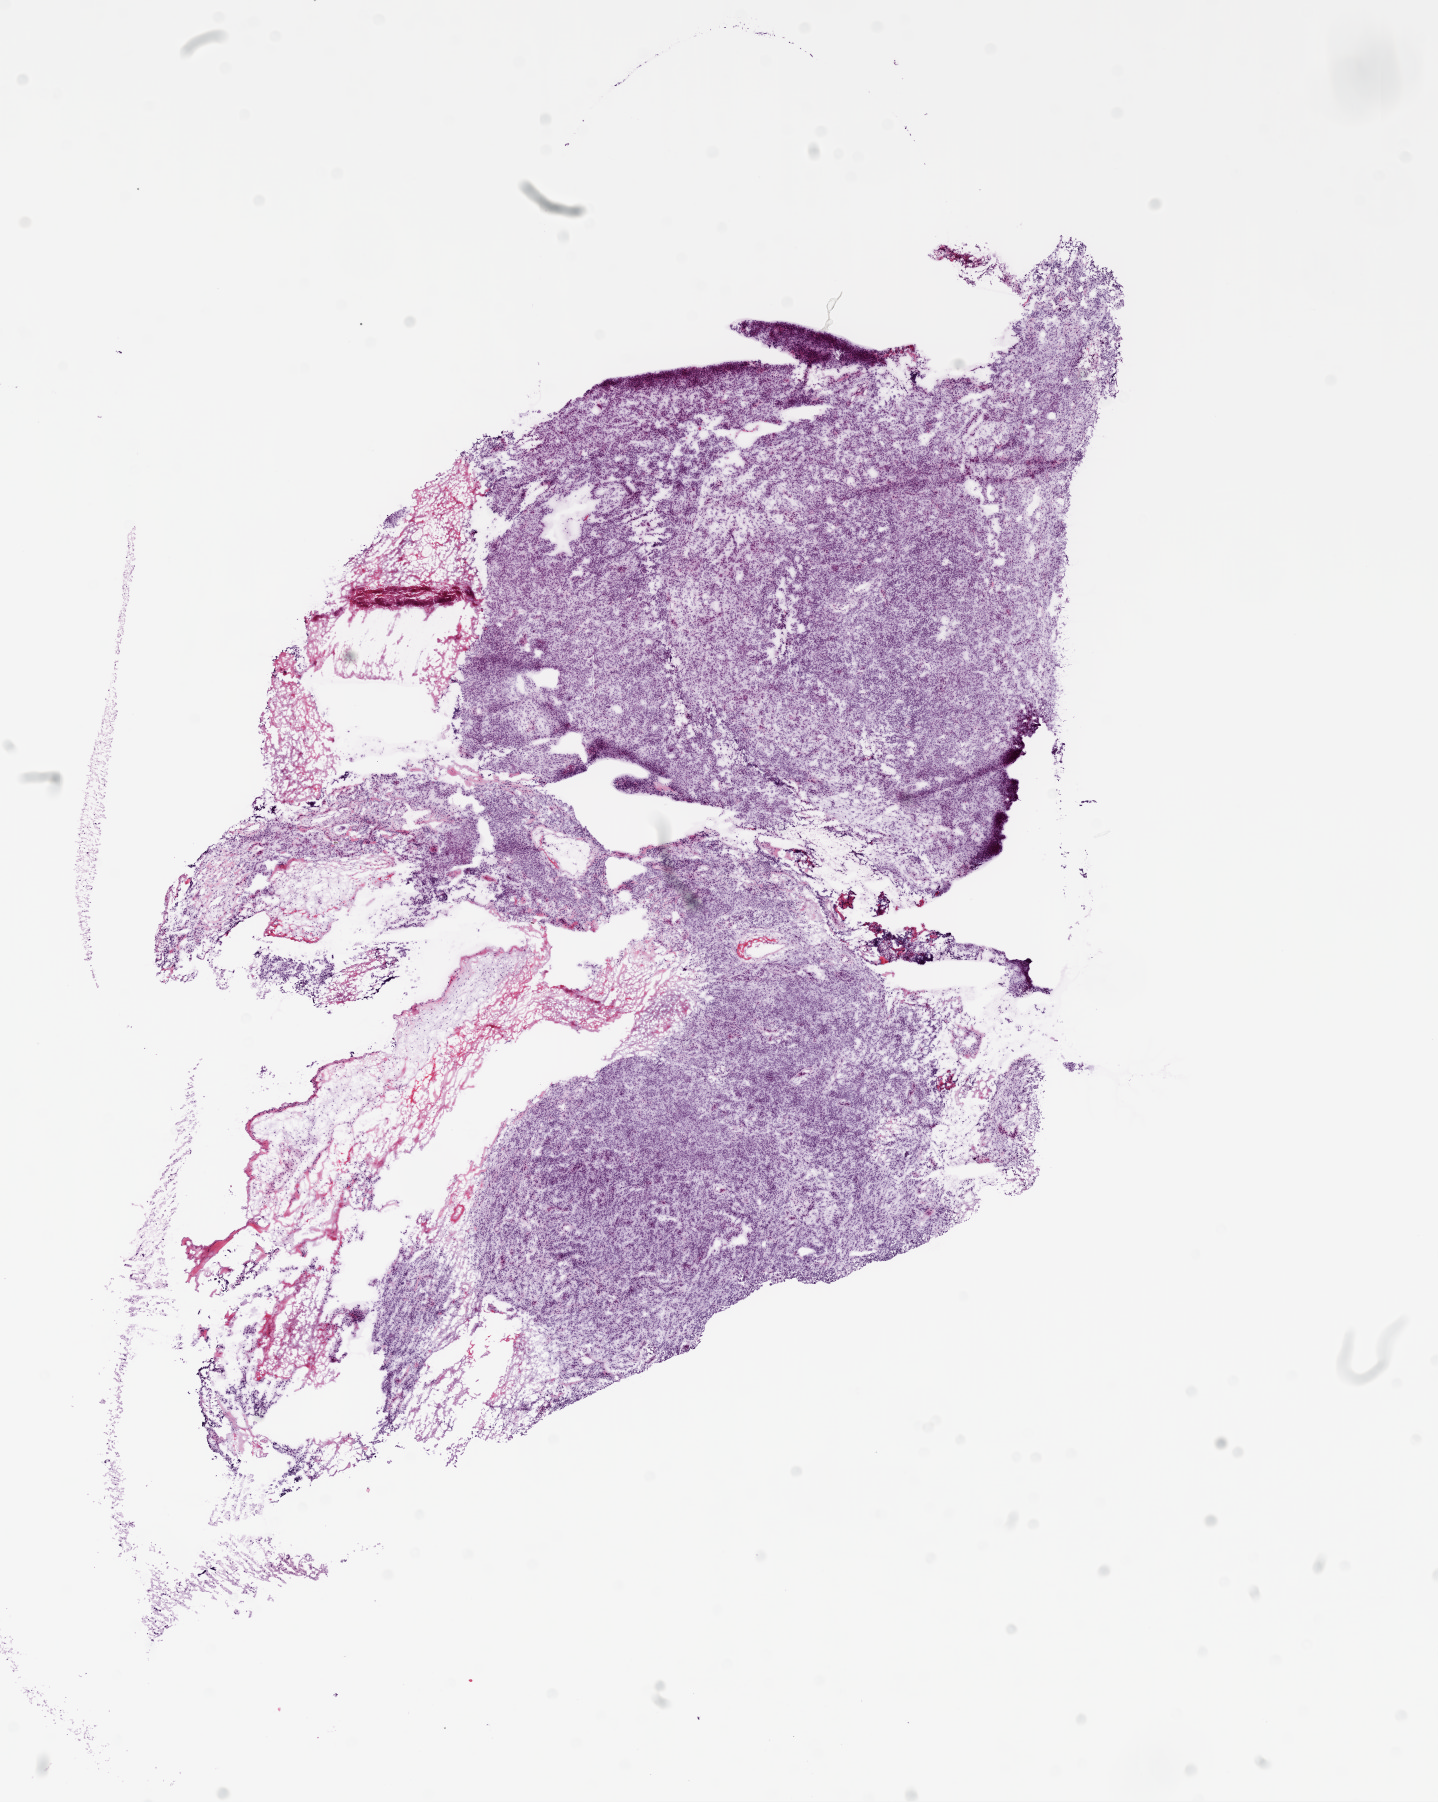
Whole-slide histology image, Hematoxylin and eosin (H&E) stained — low-resolution overview of the scanned area, about 11.6 x 14.5 mm (acquisition: 20x scan), frozen section from the top of the tissue portion, sample: primary tumour, ovary. Female, age 71 years at initial diagnosis. Slide review estimates, as recorded: tumour cells 80%, tumour nuclei 95%.
Pathologic diagnosis: Serous cystadenocarcinoma, NOS.